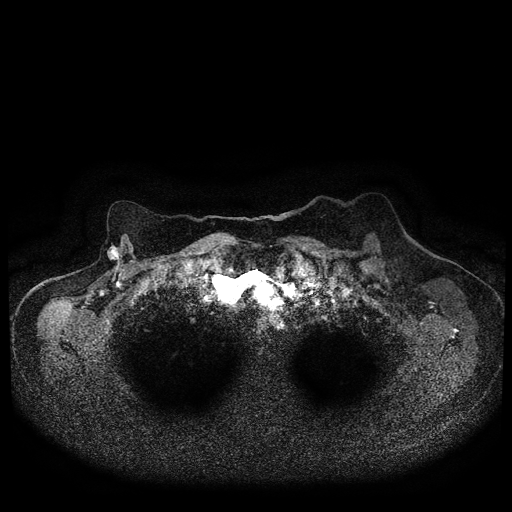
Breast MRI (dynamic contrast-enhanced, multi-phase), one axial slice; dynamic contrast-enhanced series, time point 2 of 5 at this slice position (early post-contrast); 1.5 T; TE 2.7 ms, TR 5.4 ms; 512 × 512 image matrix, field of view 340 × 340 mm. Patient: female, 72 years.
Outlined on this slice (semi-automatically segmented with operator editing):
- breast lesion (labelled 'tumour' in the annotation; benign lesions carry a separate 'benign' label): bounding box [x1, y1, x2, y2] px = [106, 243, 121, 263]